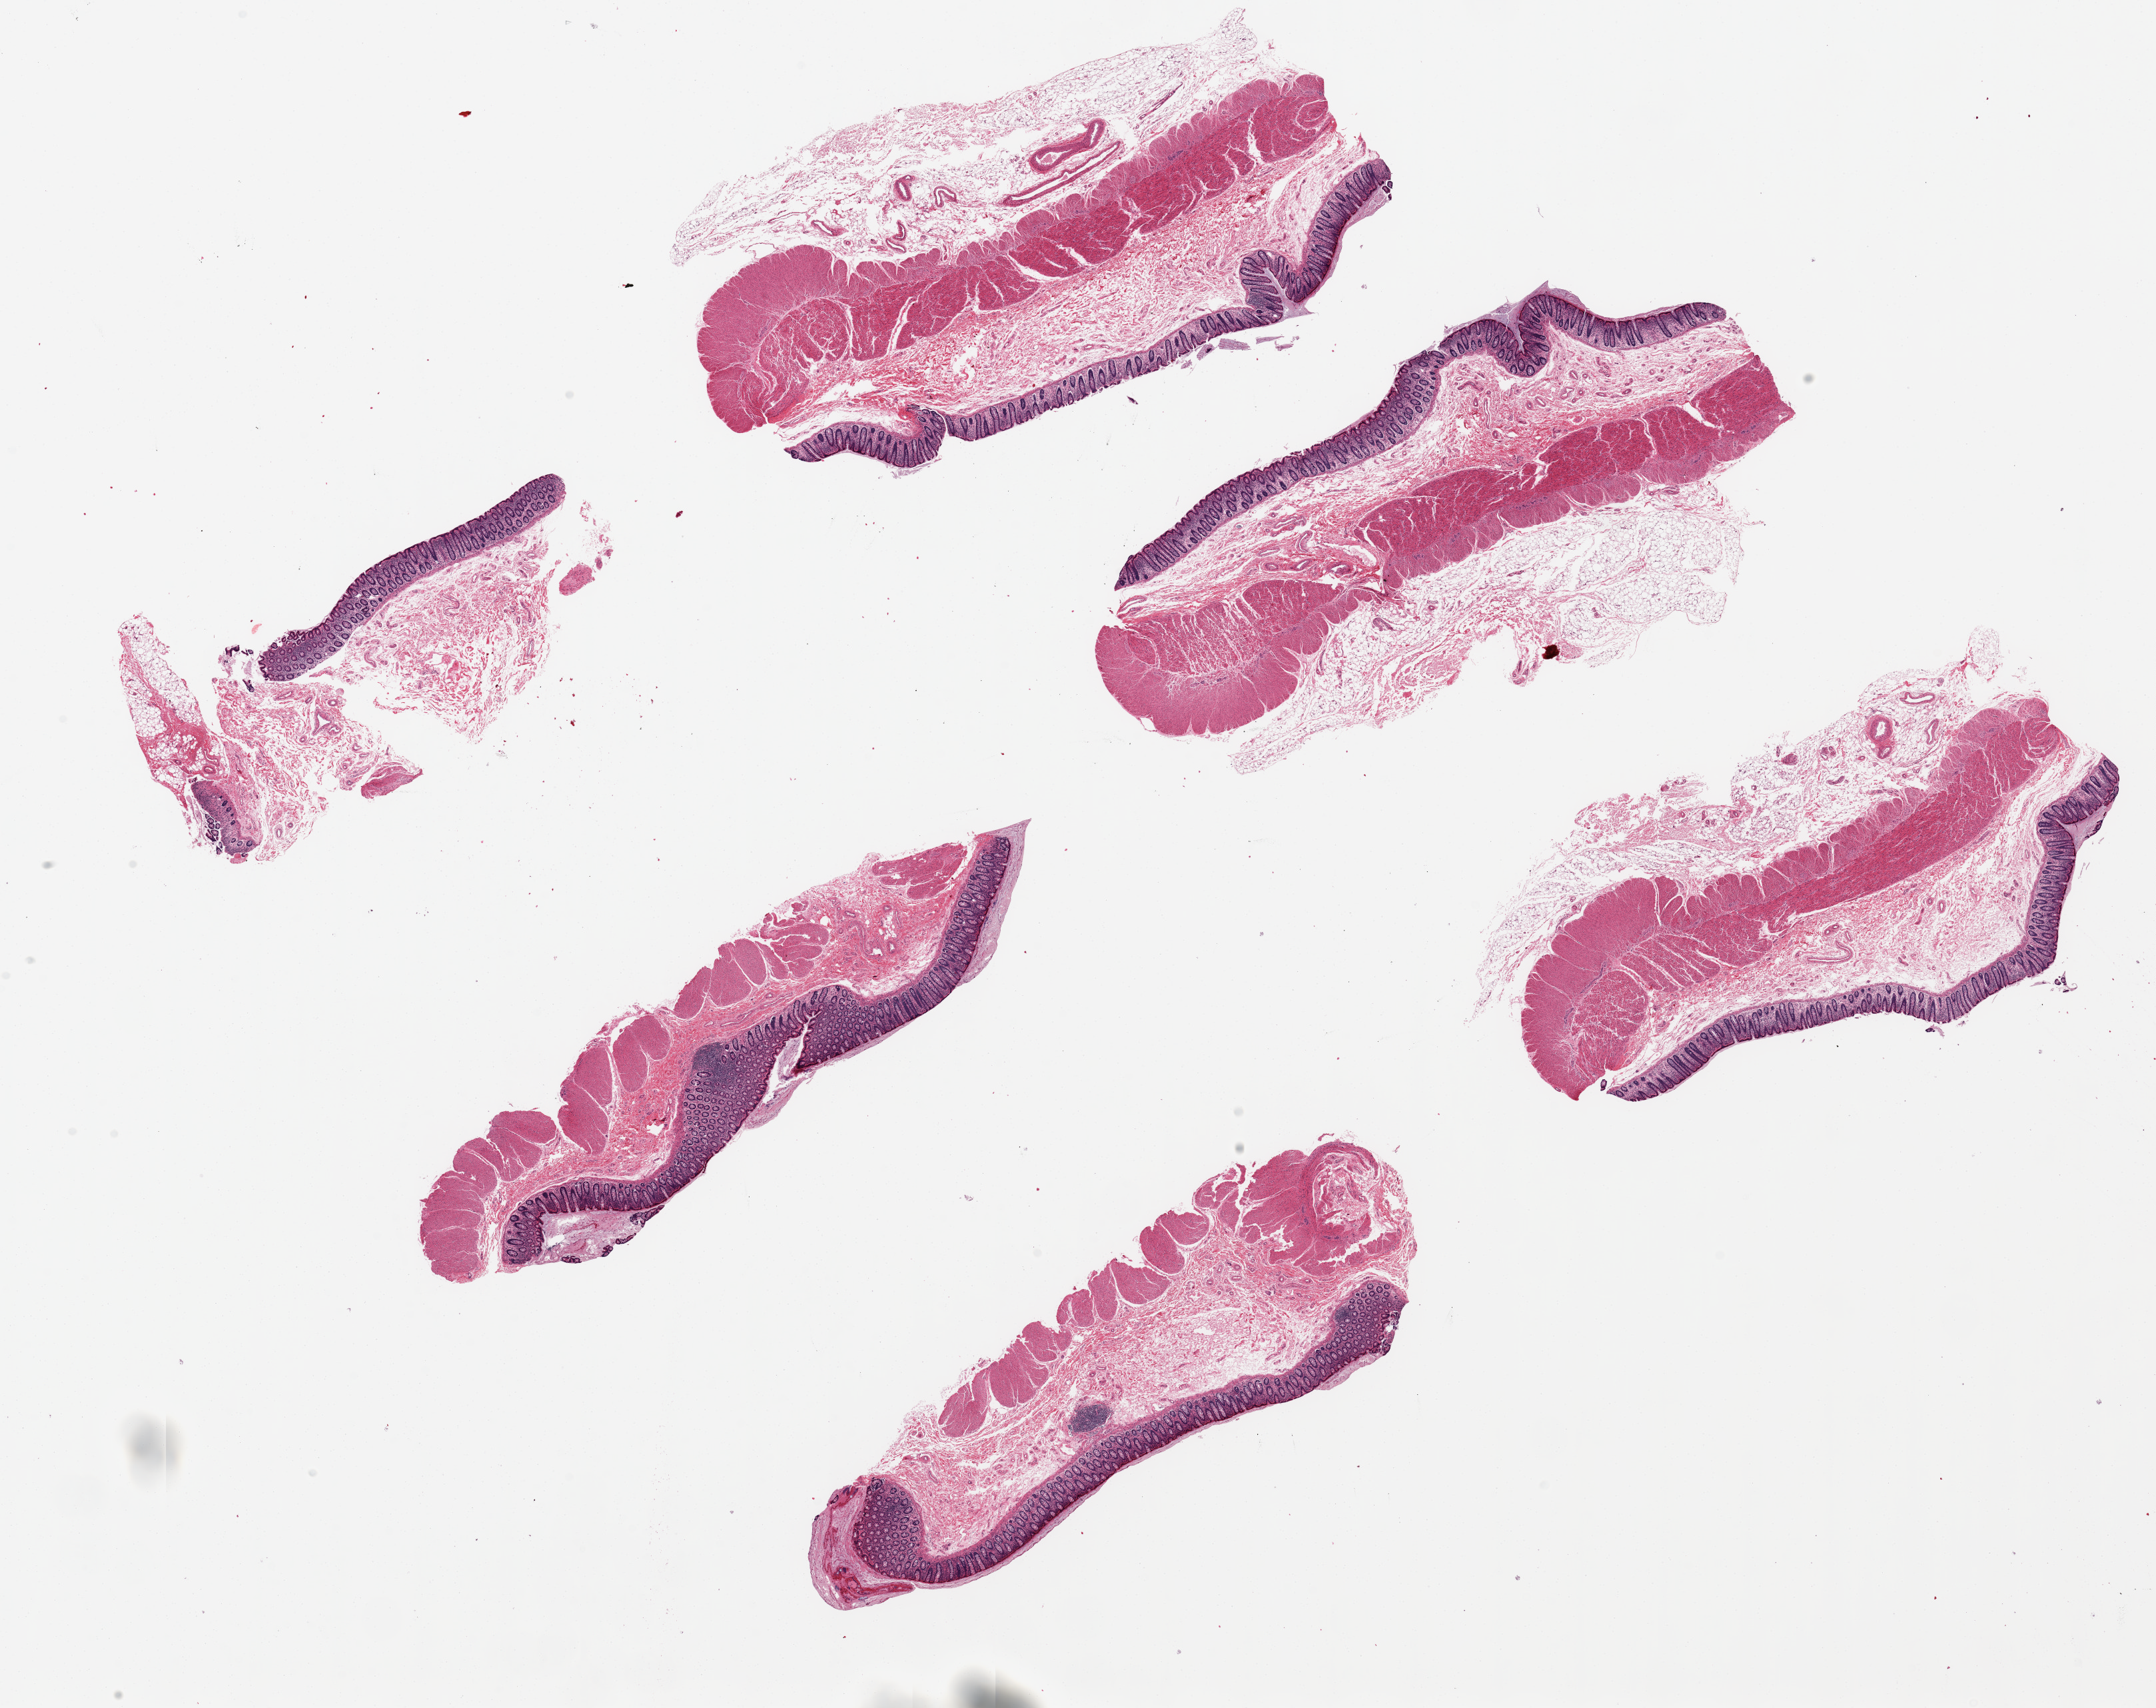
Whole-slide image, hematoxylin and eosin (H&E) stain, a low-resolution overview of the entire scanned area, about 25.6 x 20.3 mm; PAXgene-fixed paraffin-embedded (PFPE) section; section of transverse colon (target tissue); tissue donor sample. Male donor.
• pathologist's review note for this sample: 6 ~ 9x3/5mm pieces. Mucosa generally well-preserved, some autolysis superficially, is ~10% of thickness